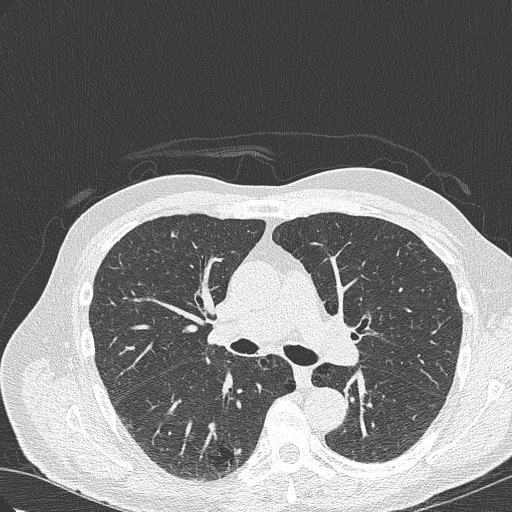
Low-dose screening chest CT, axial slice. First (baseline) screen. Lung window (W 1500 / L -600 HU). Lung (sharp) reconstruction kernel (B50f). 120 kVp. Slice 126 of 322 in the series. Male participant, aged 70 years at enrolment. Current smoker at enrolment.
Lesion marked by an expert reader, bounding box (x1, y1, x2, y2) in pixels: (200, 419, 264, 472). The screening reader recorded 4 non-calcified nodules or masses ≥4 mm on this exam (right lower lobe, right lower lobe, right upper lobe, right lower lobe); which of them this box marks is not recorded. Official screen result: positive, change unspecified: nodule(s) >= 4 mm or enlarging nodule(s), mass(es), or other non-specific abnormalities suspicious for lung cancer.